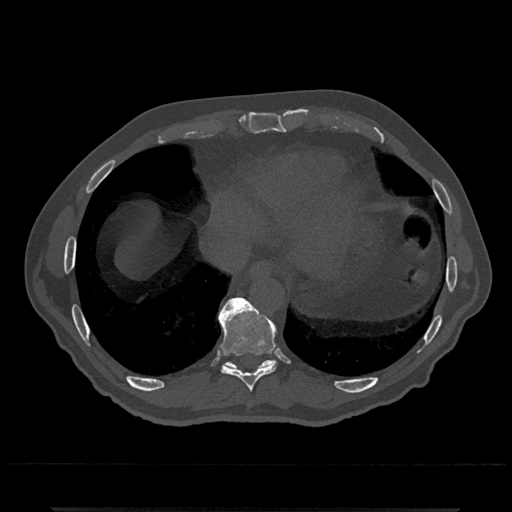
CT including the spine, one axial slice; position 597 of 797 along the scan axis; 120 kVp; bone window (W 1800 / L 400 HU); 512 × 512 image matrix. Patient: male, 67 years. Case-level facts recorded for this patient, not image findings: primary cancer: prostate.
Annotated regions visible in this slice (semi-automatically segmented with operator editing):
- T10 vertebra: bounding box [x1, y1, x2, y2] px = [224, 297, 276, 368]
- T9 vertebra: [218, 297, 277, 392]